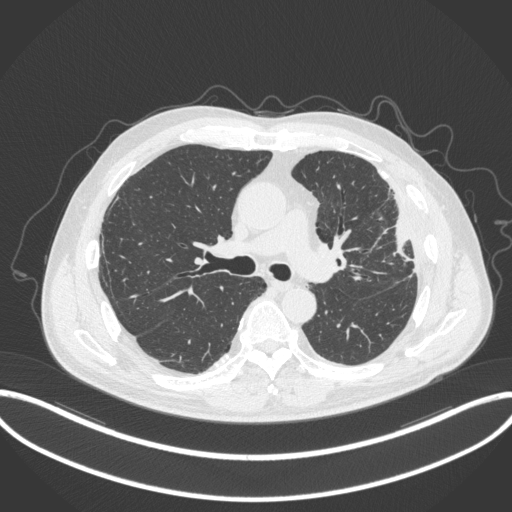
Chest CT, one axial slice; position 210 of 382 along the scan axis; reconstruction kernel B31f; lung window (W 1500 / L -600 HU); 512 × 512 image matrix, field of view 415 × 415 mm. Patient: male, 64 years. From the clinical record (not read from this slice): clinical TNM (as recorded): T4 N1 M0; histopathological grade: G3.
Structures marked on this image (rectangle marked by the reading radiologist):
- lung tumour (recorded histology: adenocarcinoma): bounding box (x1, y1, x2, y2) in pixels: (386, 210, 419, 267)